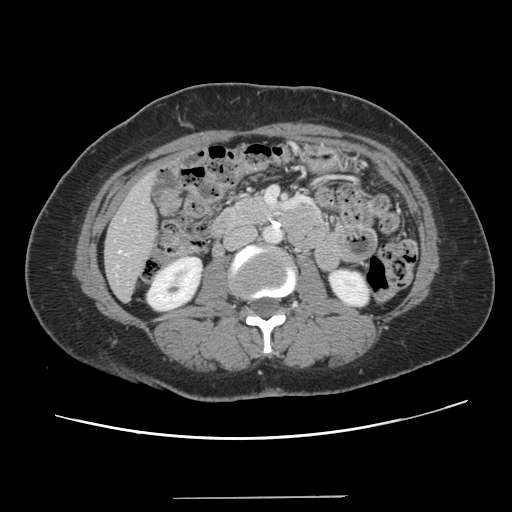
Contrast-enhanced abdominal CT, one axial slice. Slice 37 of 141 in the series (ordered by position). 120 kVp. Soft-tissue window (W 400 / L 40 HU). 2.5 mm slice thickness. 512 × 512 image matrix. Female patient, age 53 years. Case-level facts recorded for this patient, not image findings: diagnosis: colorectal cancer liver metastases, imaged before liver resection; multiple liver metastases: no; largest metastasis: 14.5 cm; chemotherapy before resection: yes.
Structures marked on this image (expert manual segmentation):
- liver: bounding box [x1, y1, x2, y2] px = [105, 174, 157, 300]
- planned liver remnant (the part of the liver to remain after resection): [105, 213, 157, 300]